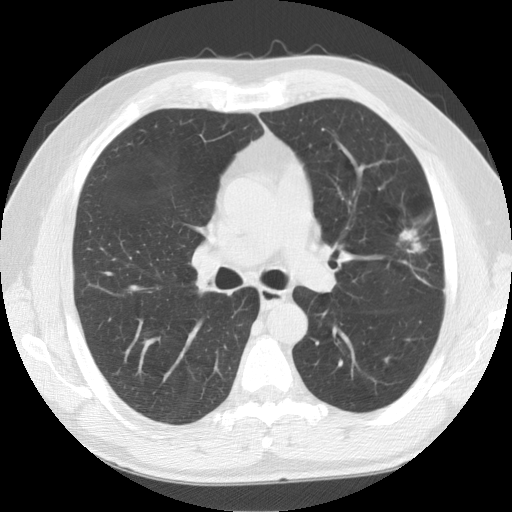
Low-dose screening chest CT, one axial slice; slice 90 of 141 in the series (ordered by position); reconstruction kernel STANDARD; lung window (W 1500 / L -600 HU); 512 × 512 image matrix, field of view 360 × 360 mm.
Structures marked on this image (expert manual segmentation):
- lesion 1 (tumor, upper lobe of left lung): bounding box [x1, y1, x2, y2] px = [400, 229, 423, 253]